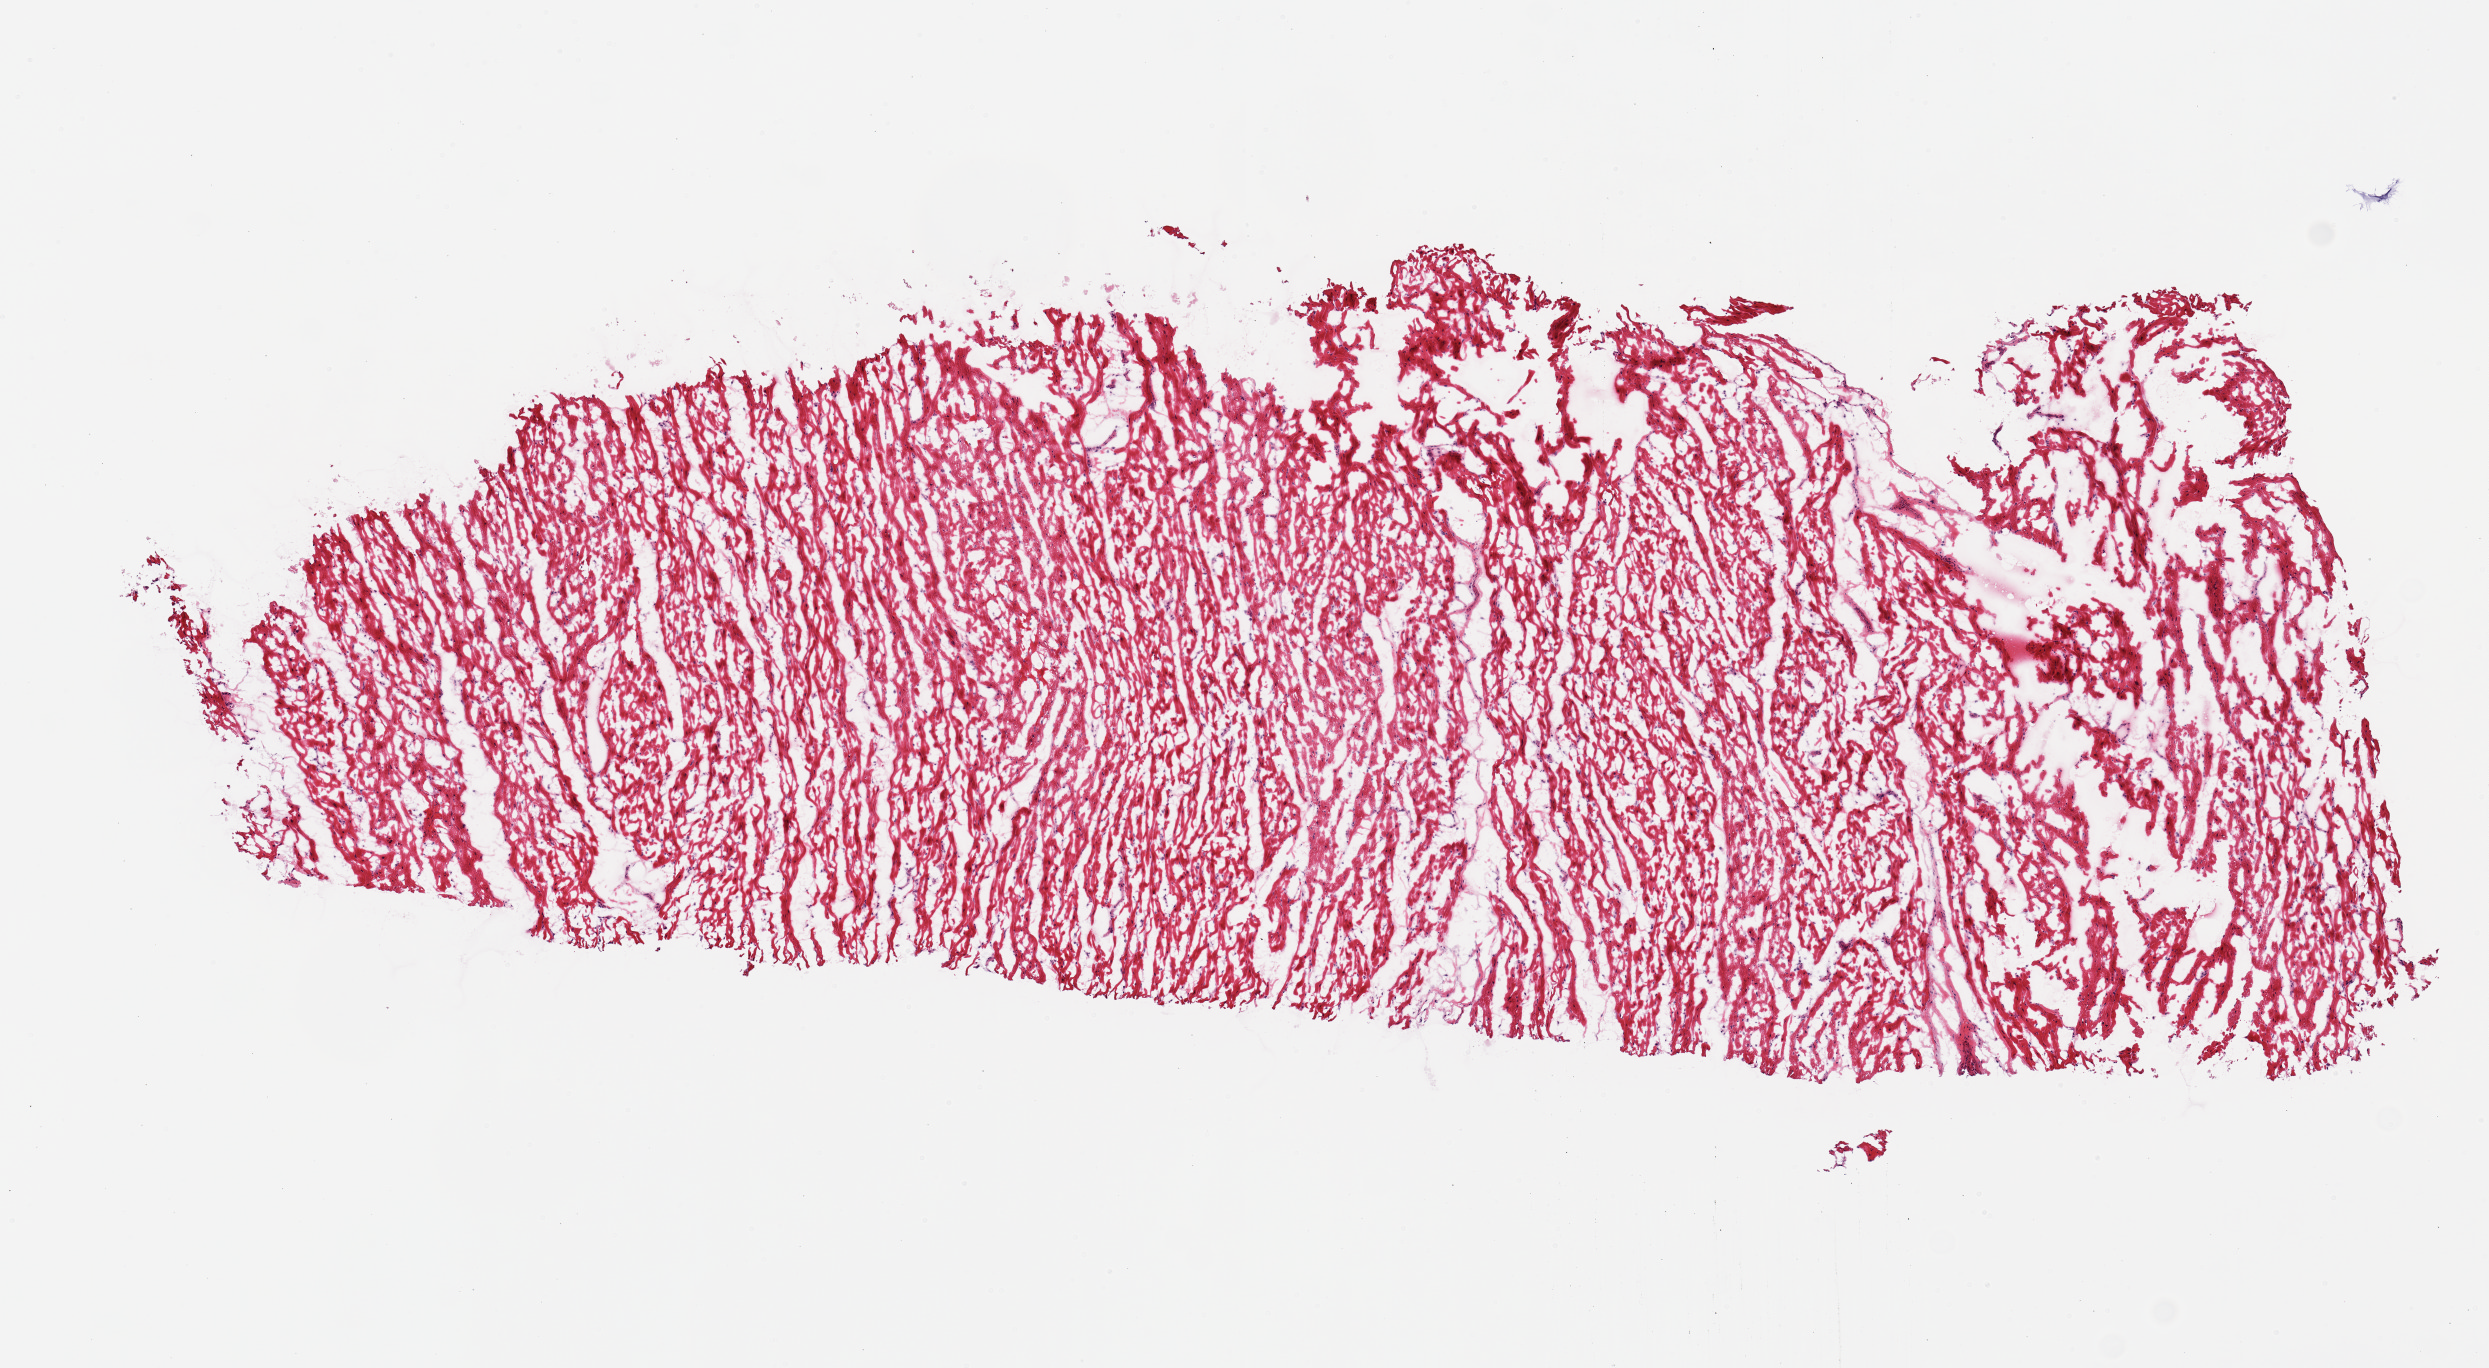
H&E whole-slide image — low-resolution overview of the scanned area, about 9.8 x 5.4 mm. Female donor.
Specimen: frozen section; target tissue: heart; tissue donor sample.